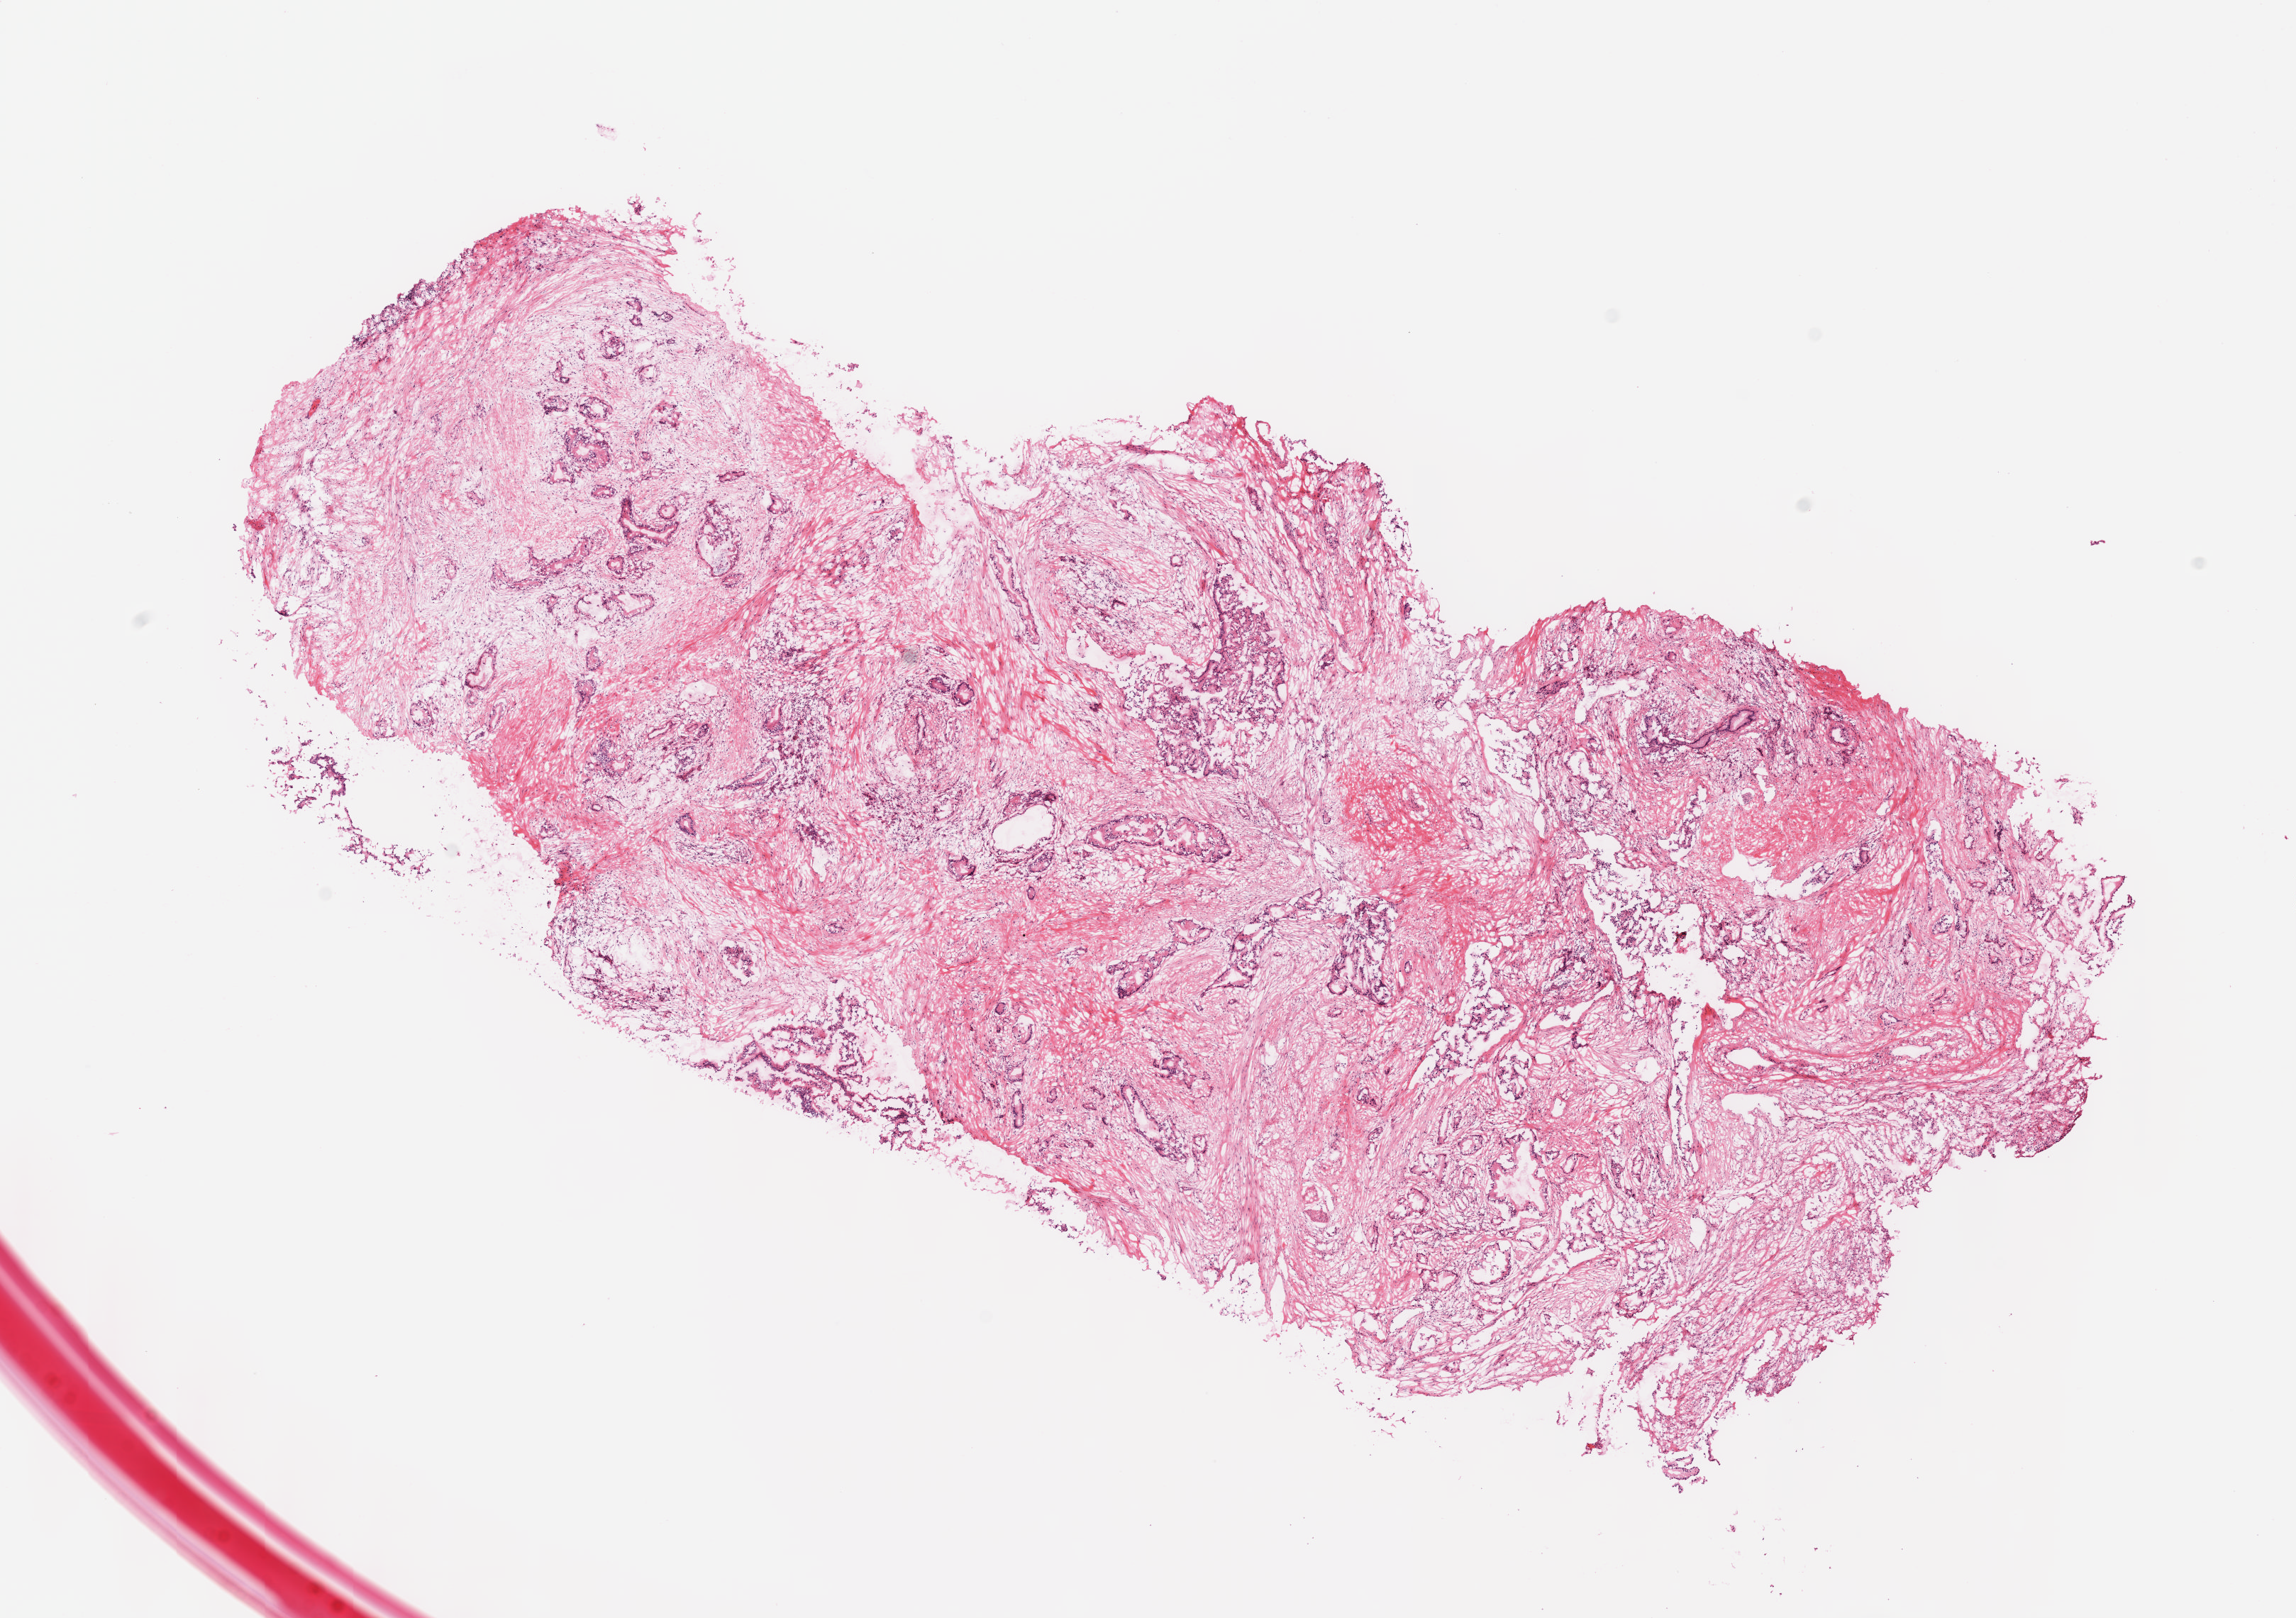
Whole-slide histology image, Hematoxylin and eosin (H&E) stained — a low-resolution overview of the entire scanned area, about 13.1 x 9.2 mm (slide scanned at 40x). Formalin-fixed paraffin-embedded (FFPE) diagnostic section. Primary tumour sample from the pancreas. Male, age 65 years at initial diagnosis. Histologic grade: G2 (moderately differentiated).
Pathologic diagnosis: Infiltrating duct carcinoma, NOS (head of pancreas). AJCC pathologic stage: IIB (7th edition).